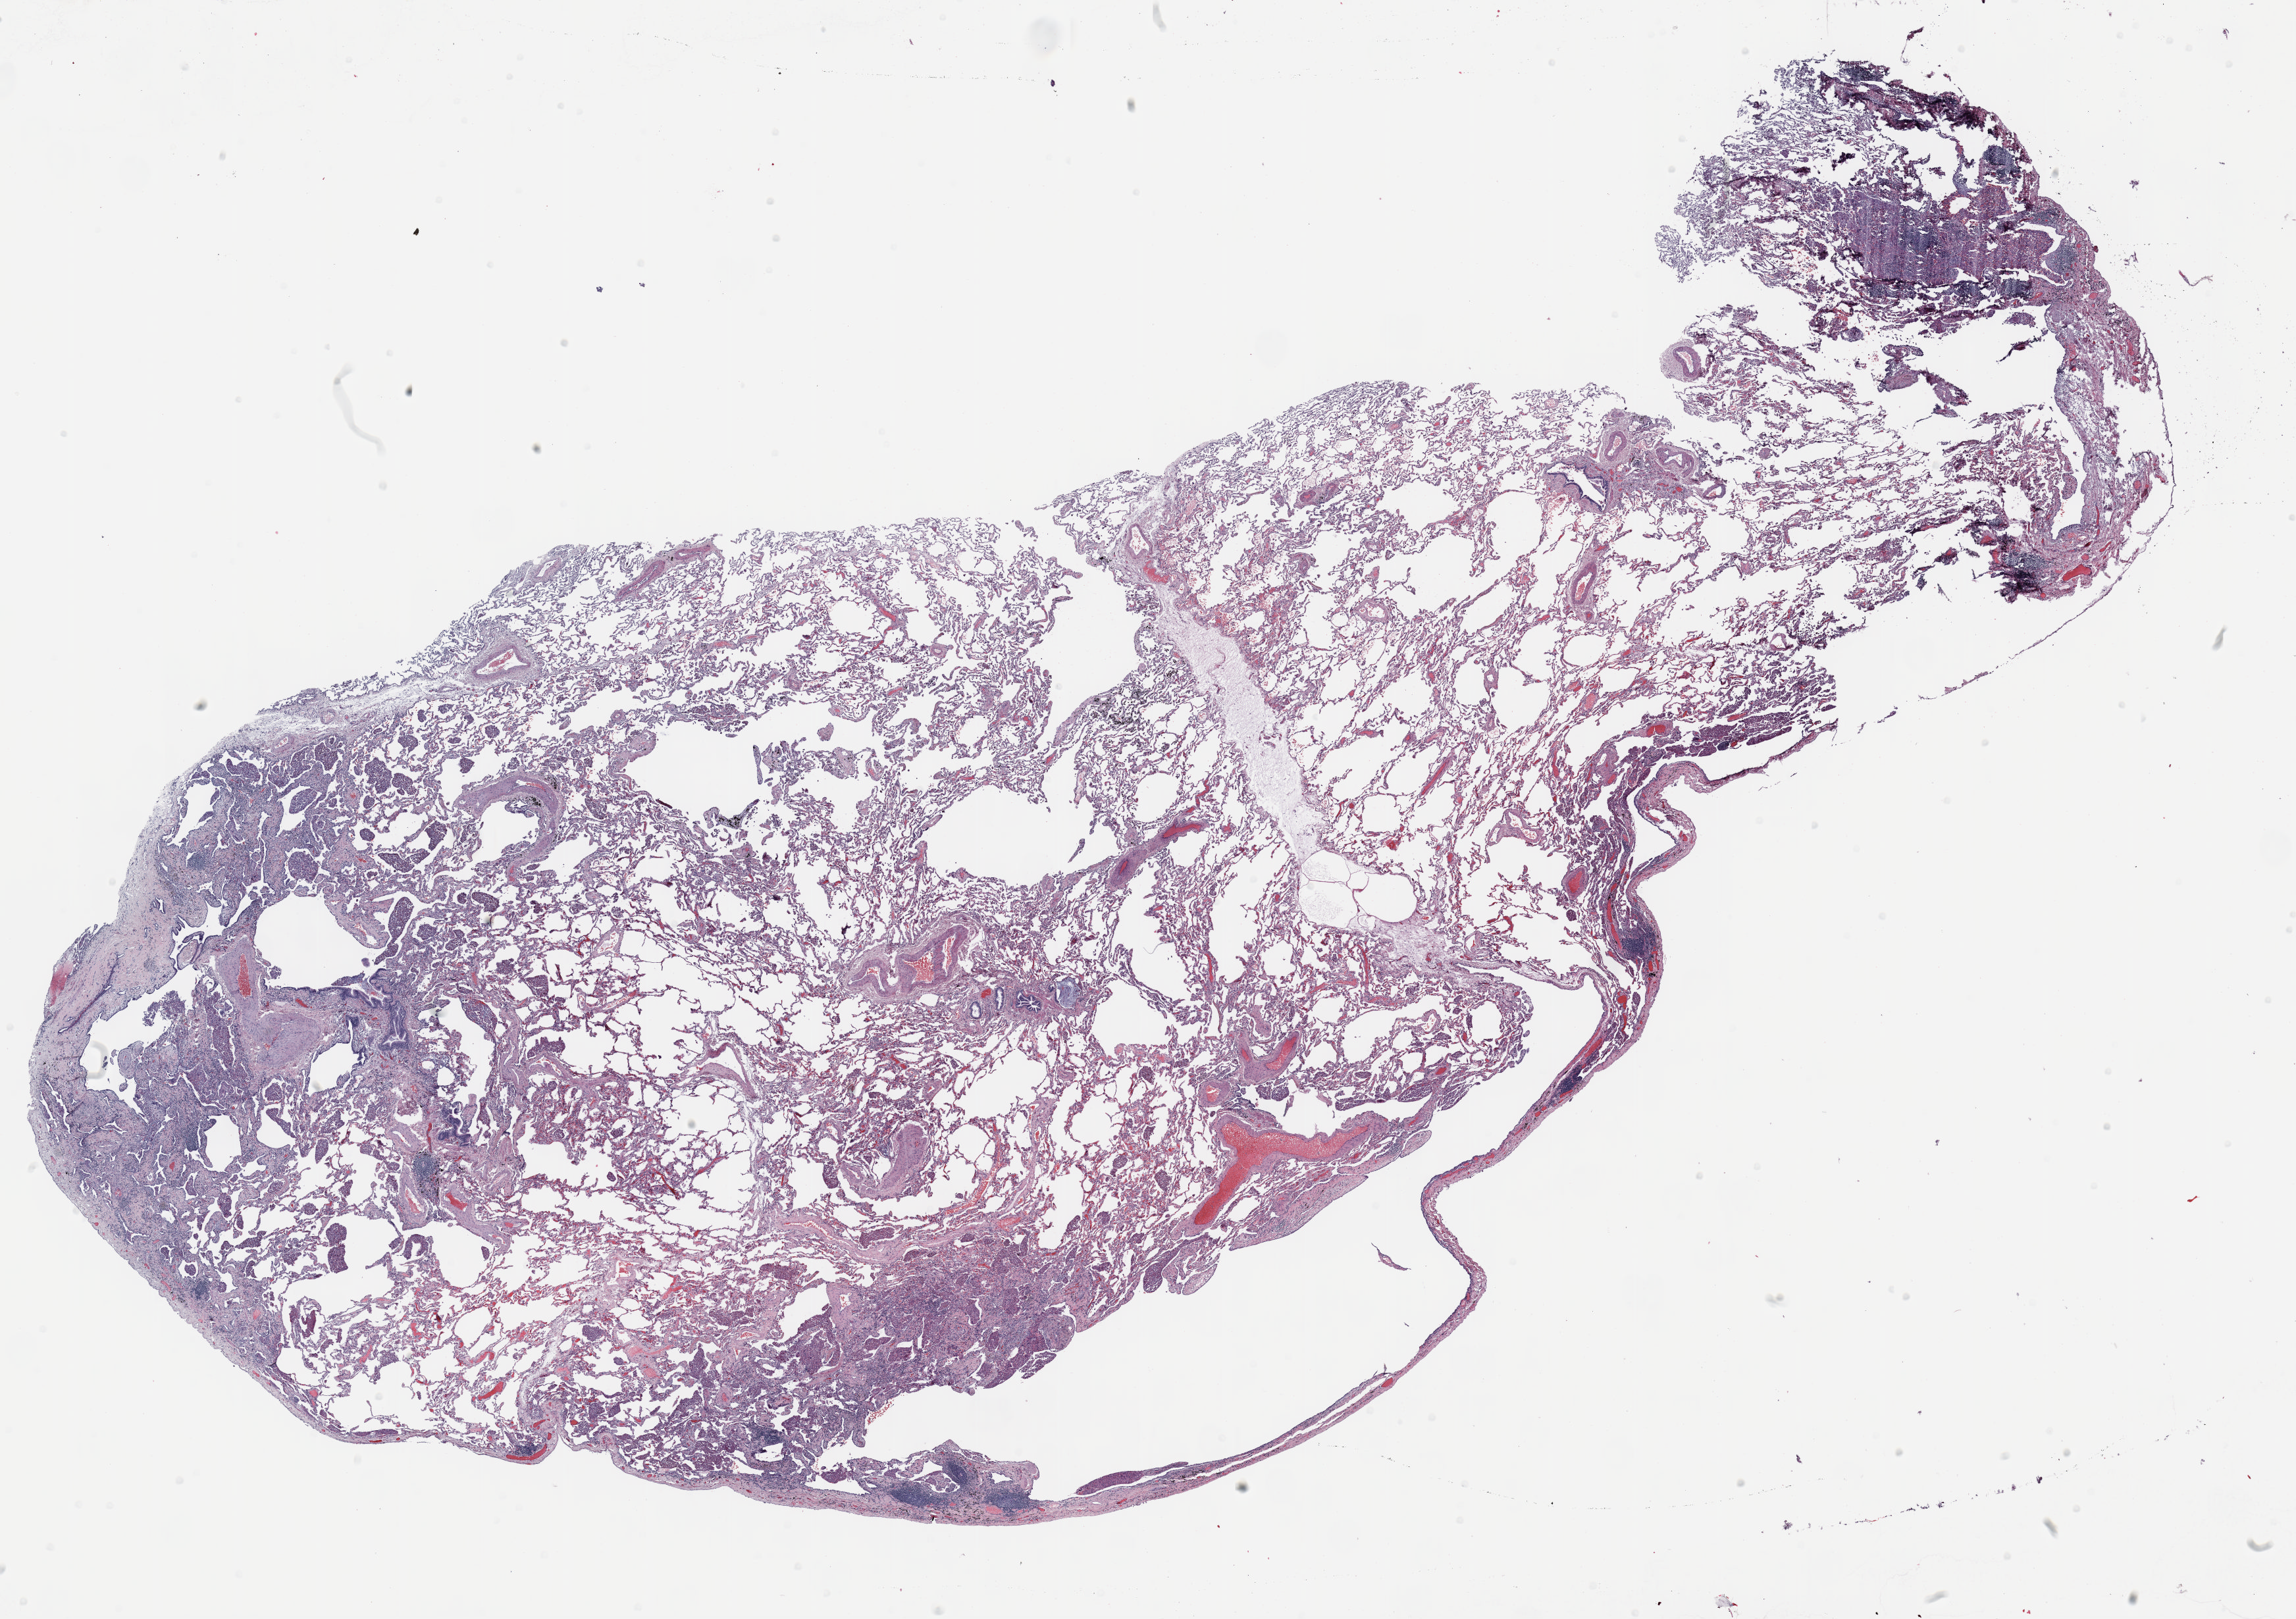
Hematoxylin and eosin (H&E) stained whole-slide image, shown as a low-resolution overview of the whole scanned area (about 28.0 x 19.8 mm, slide scanned at 20x), FFPE section, lung. Male, age 59 at enrolment.
Participant's lung-cancer diagnosis: Bronchiolo-alveolar adenocarcinoma, NOS.